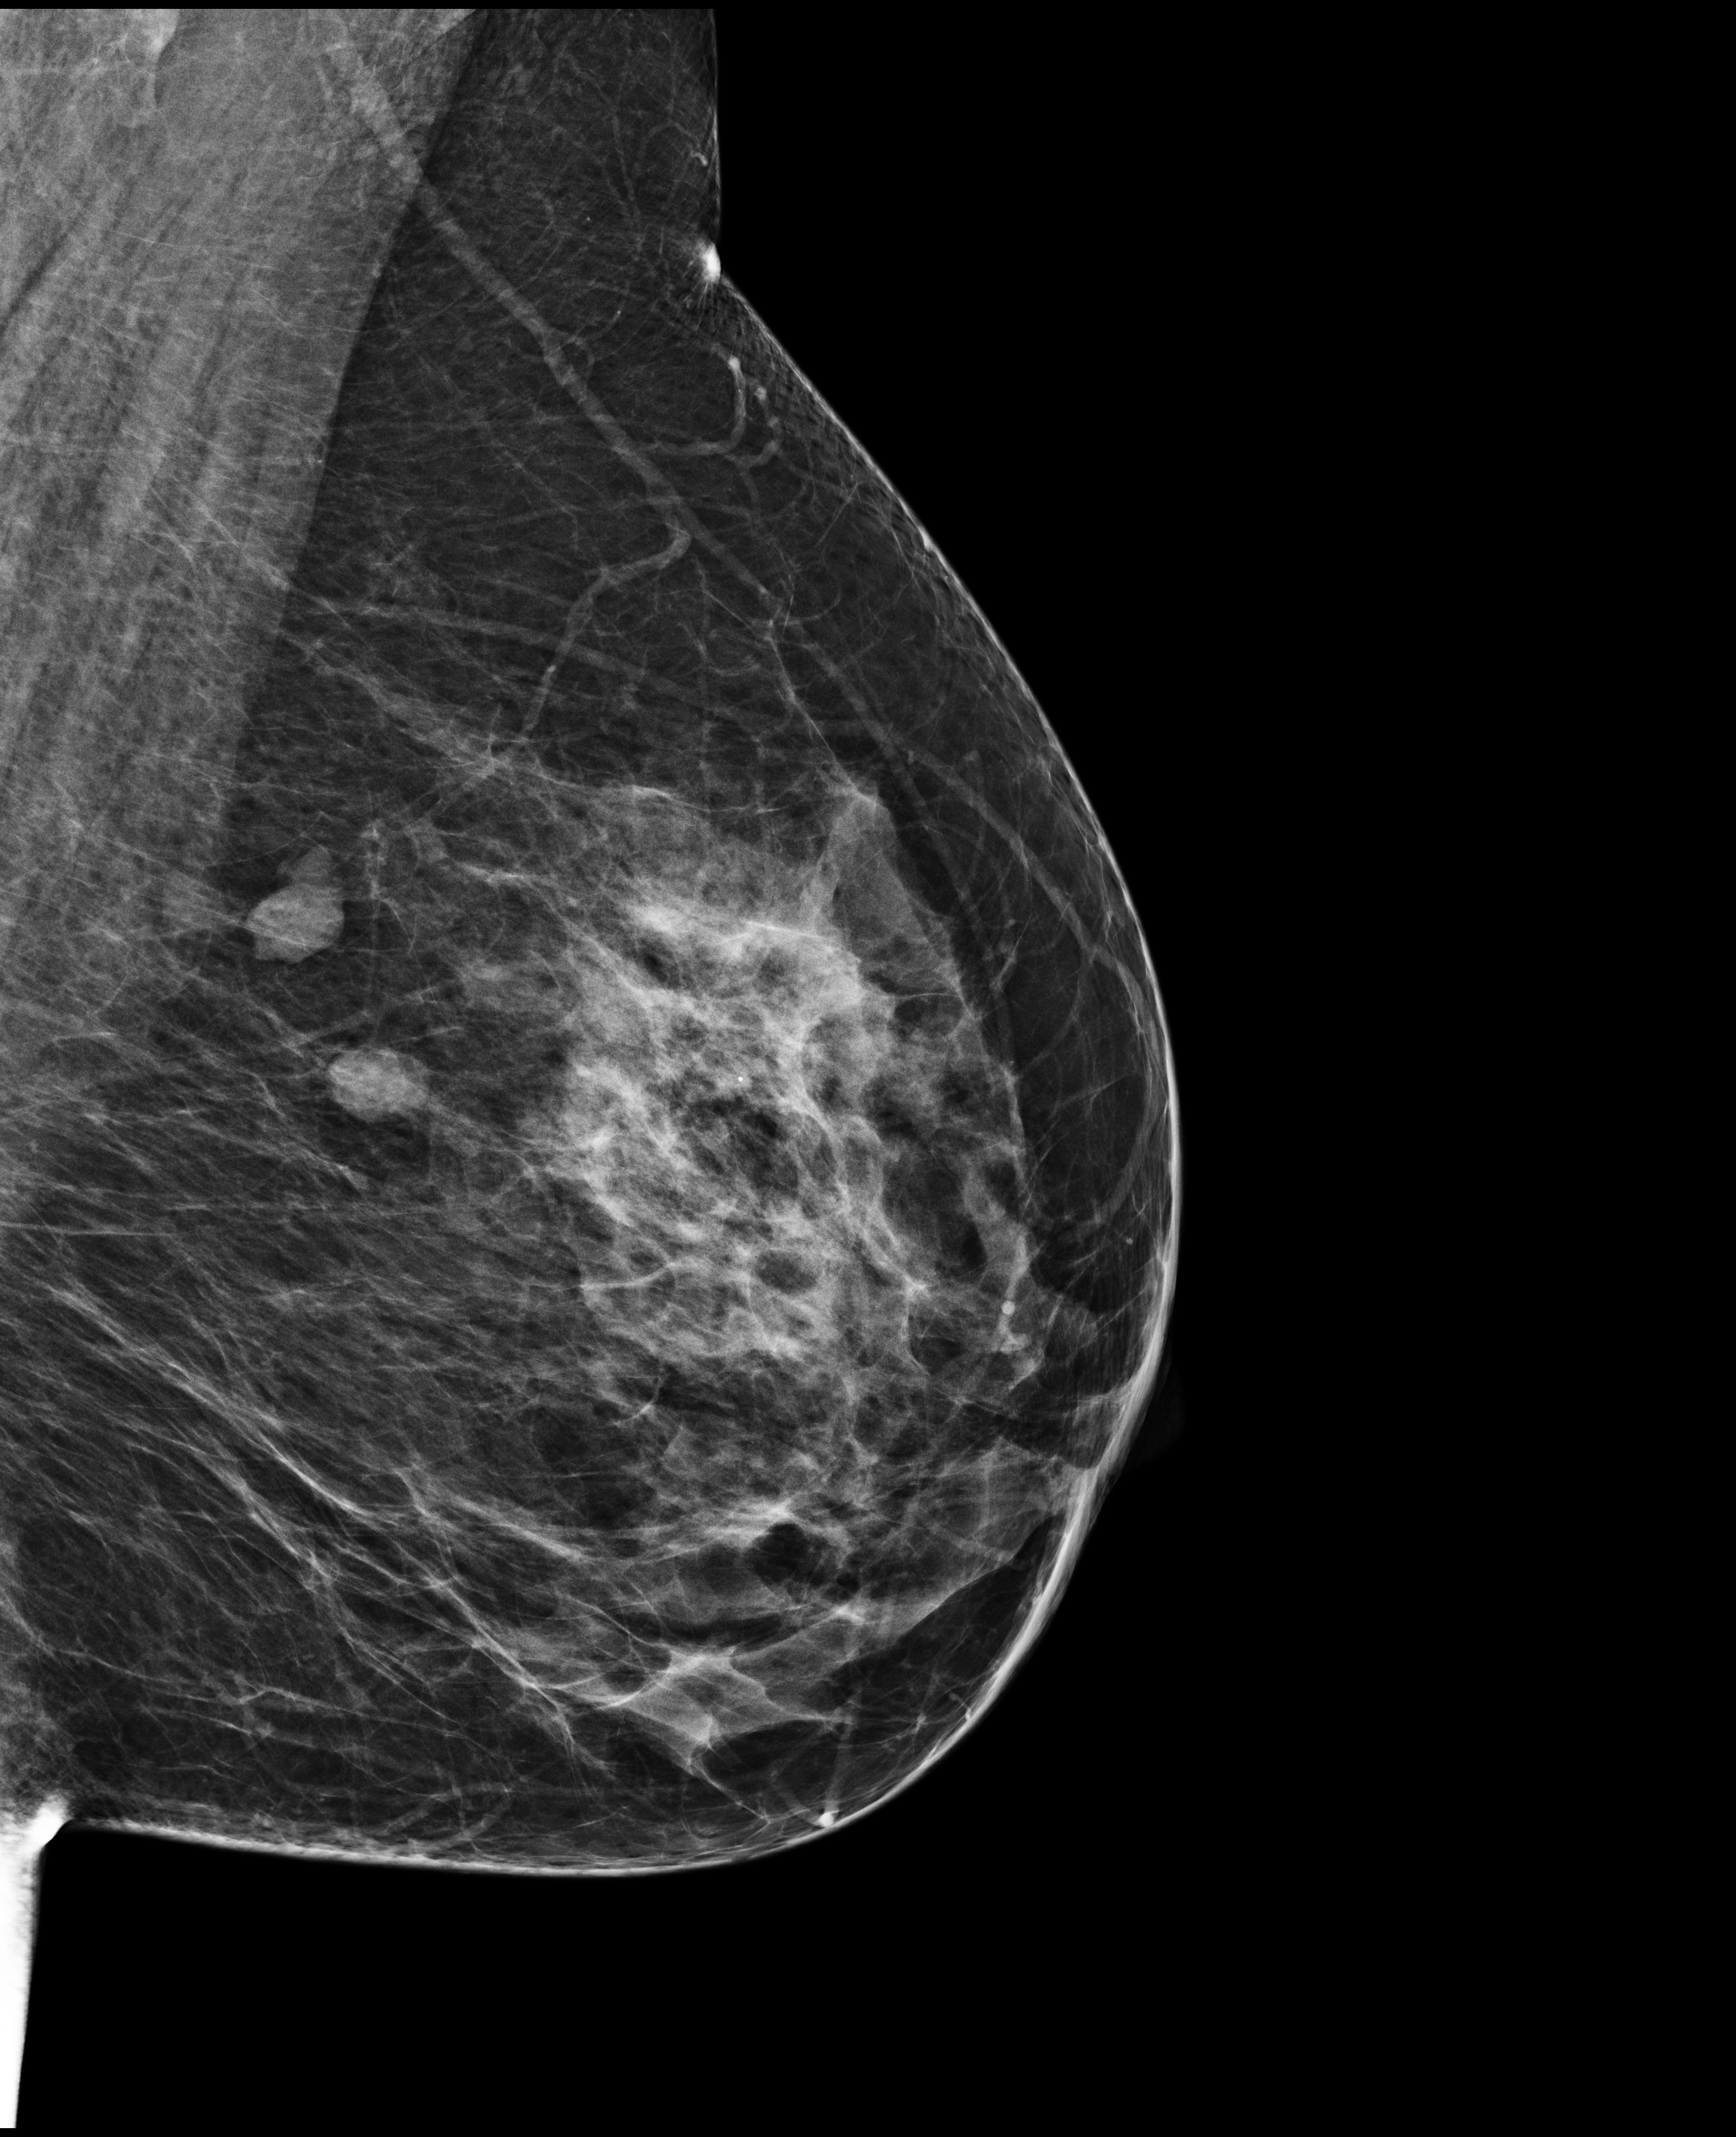
Annual screening mammography examination. Female patient, age 49 years.
Image type: full-field digital mammogram. Breast: left. Projection: mediolateral oblique (MLO) view.